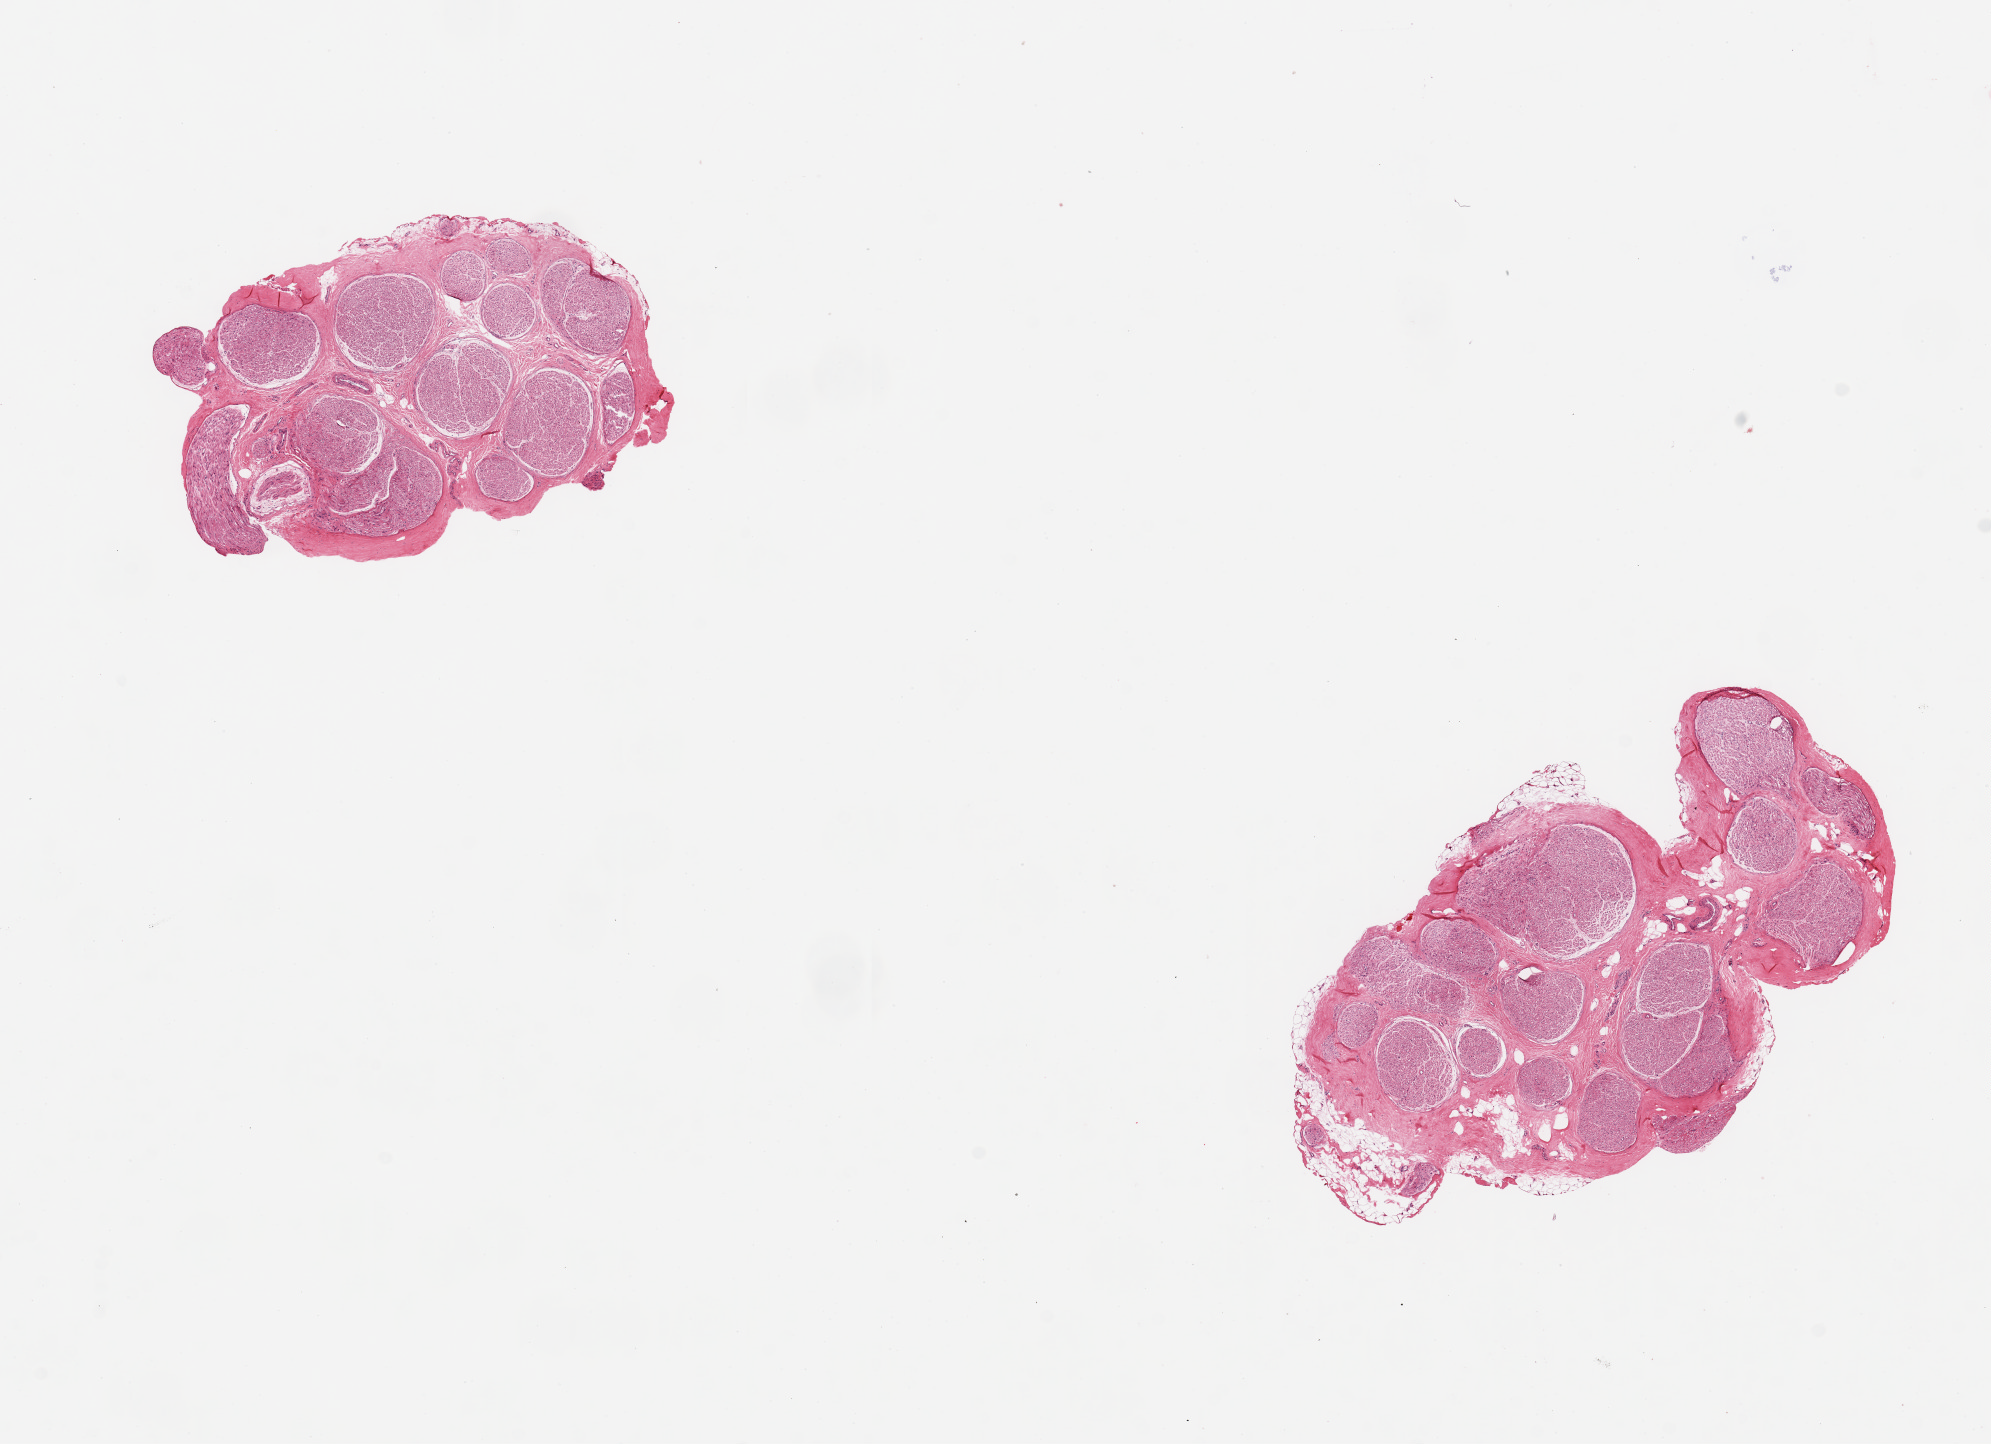
Haematoxylin and eosin whole-slide image, whole scanned area (about 15.8 x 11.4 mm) shown as a low-resolution overview, PAXgene-fixed, paraffin-embedded tissue, section of tibial nerve (target tissue), tissue donor sample. Male donor.
• review note (as recorded): 2 pieces ~4mm d. Good clean specimens